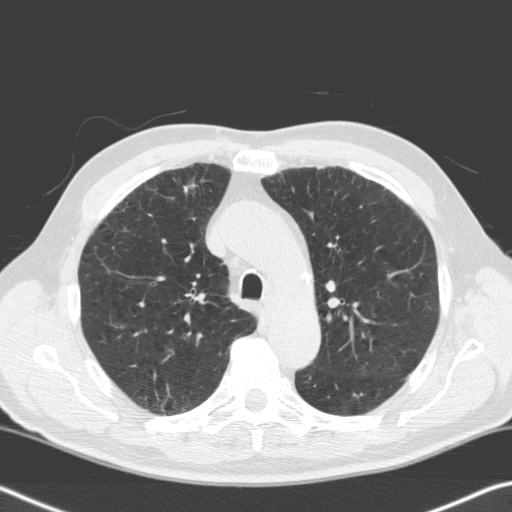
Low-dose screening chest CT, one axial slice; position 125 of 170 along the scan axis; 120 kVp; lung window (W 1500 / L -600 HU); 3.2 mm slice thickness; 512 × 512 image matrix, field of view 343 × 343 mm.
Structures marked on this image (manually delineated by an expert):
- lesion 1 (tumor, upper lobe of right lung): bounding box (x1, y1, x2, y2) in pixels: (184, 183, 196, 193)